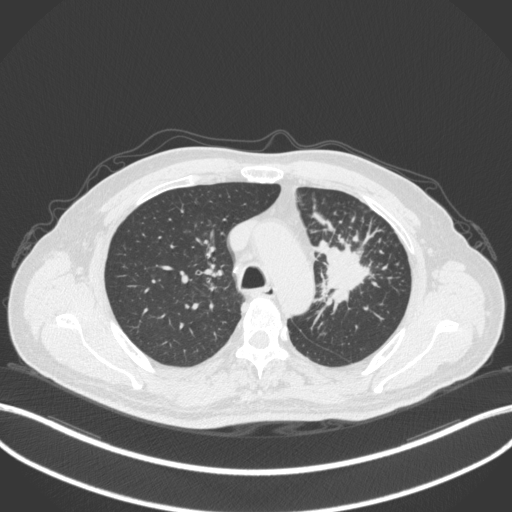
Chest CT, one axial slice; position 258 of 386 along the scan axis; reconstruction kernel B31f; 120 kVp; lung window (W 1500 / L -600 HU); 1 mm slice thickness; 512 × 512 image matrix, field of view 400 × 400 mm. Patient: male, 69 years. Case-level facts recorded for this patient, not image findings: clinical TNM (as recorded): T2a N2 M0; histopathological grade: G2-3.
Annotated regions visible in this slice (rectangle marked by the reading radiologist):
- lung tumour (recorded histology: adenocarcinoma): bounding box (x1, y1, x2, y2) in pixels: (315, 236, 376, 313)